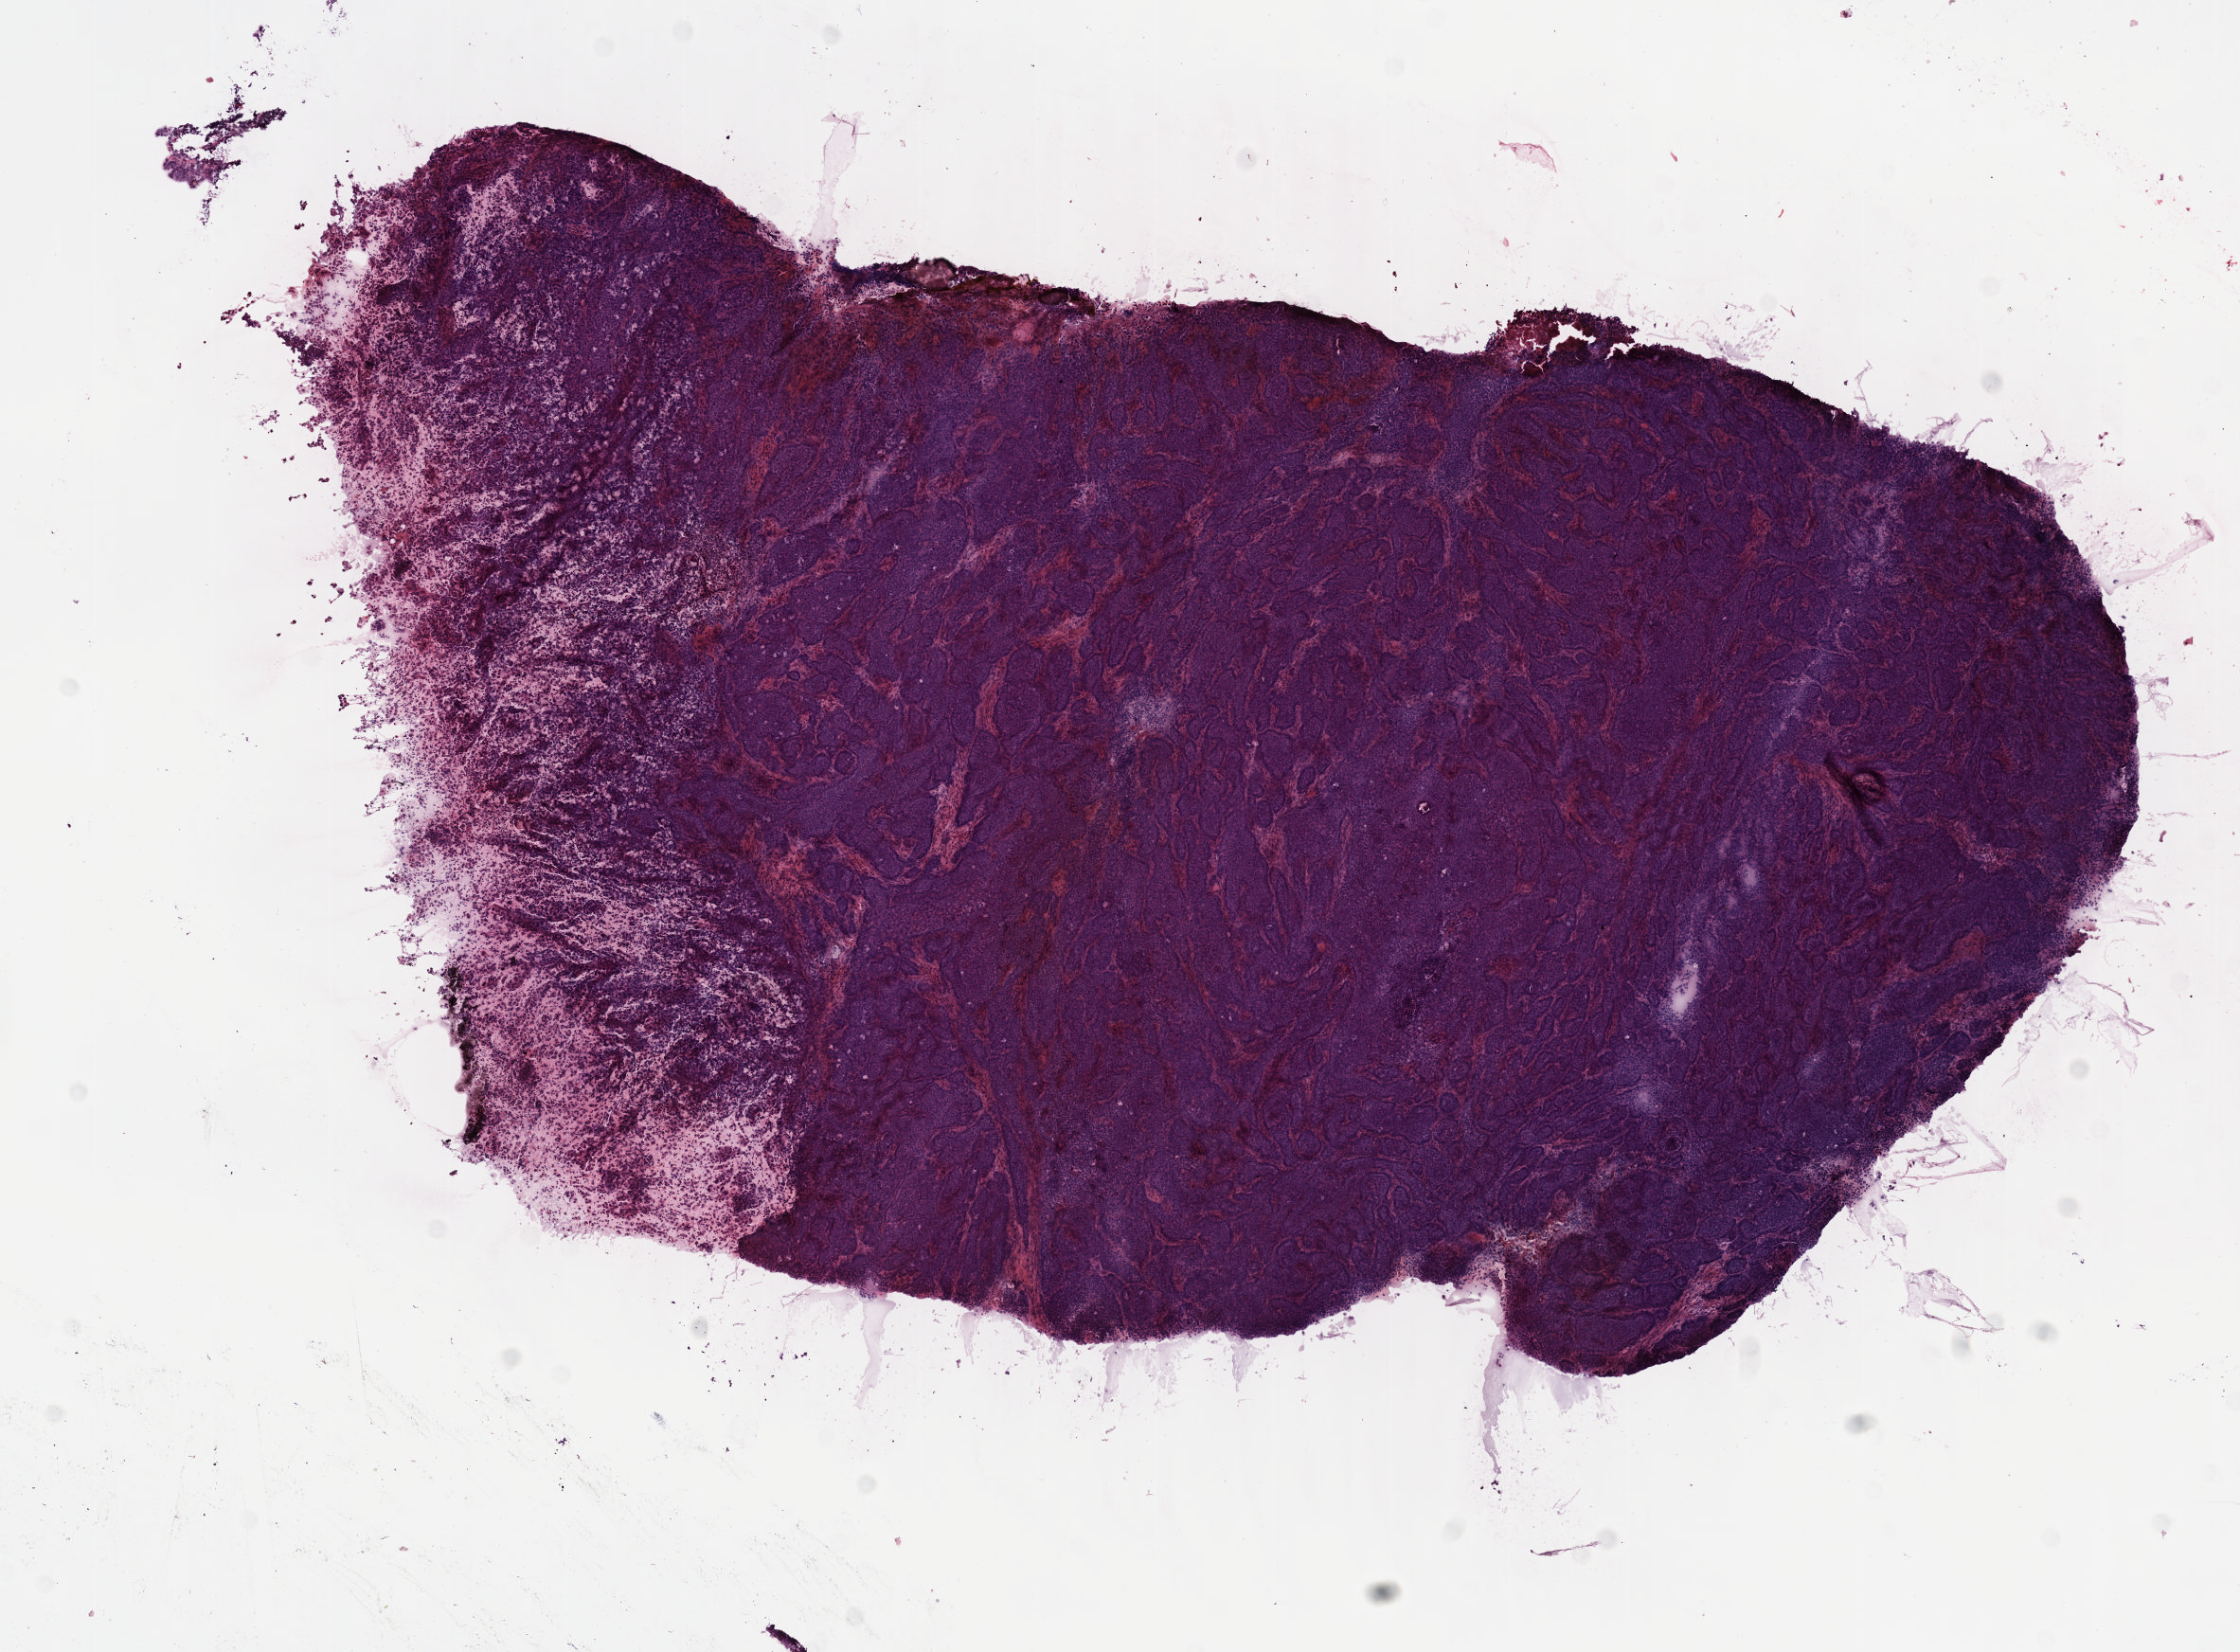
Digitized H&E tissue section (whole slide), a low-resolution overview of the entire scanned area, about 9.6 x 7.1 mm (from a 40x scan), frozen section from the top of the tissue portion, primary tumour sample from the esophagus. Male patient; age at initial diagnosis 70 years. Histologic grade: G3 (poorly differentiated). Slide review estimates, as recorded: tumour cells 77%, tumour nuclei 90%, normal cells 0%, stromal cells 20%, necrosis 3%. Infiltration values recorded for this section: lymphocyte infiltration 6%, monocyte infiltration 1%, neutrophil infiltration 2%.
- AJCC pathologic stage: III (5th edition)
- histologic diagnosis: Adenocarcinoma, NOS (lower third of esophagus)
- lymph nodes positive (case pathology): 5 of 22 examined